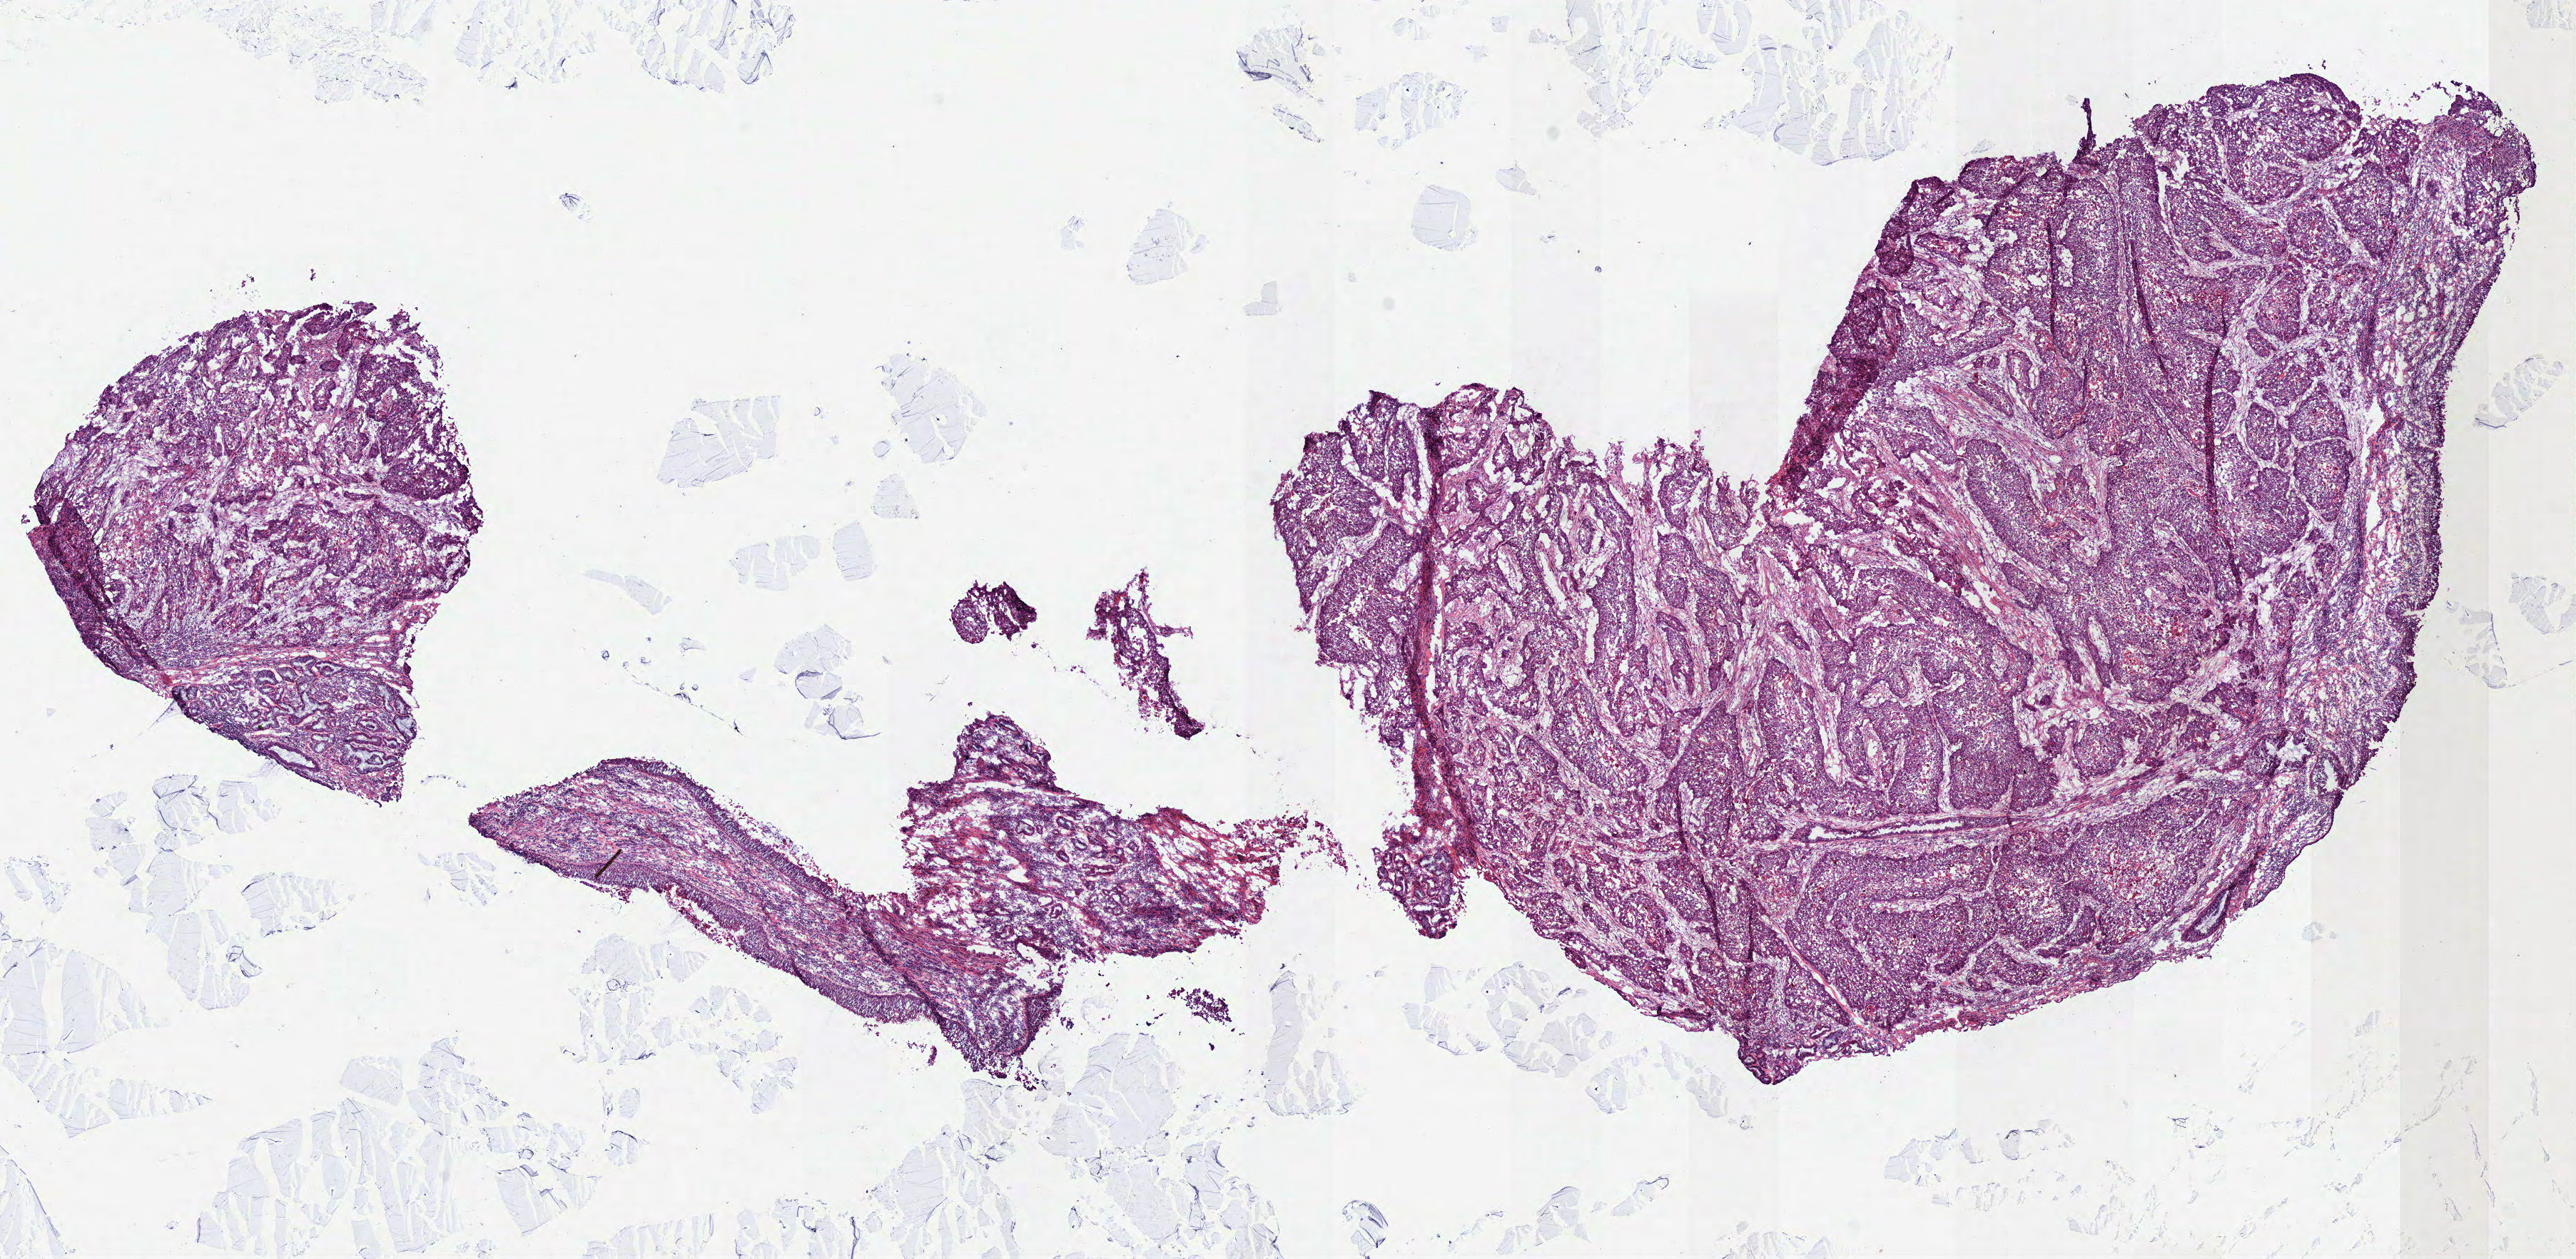
Whole-slide histology image, H&E-stained — low-resolution overview of the scanned area, about 14.2 x 6.9 mm, frozen section, head and neck, primary tumour sample. Patient: male, age at initial diagnosis 47 years. Histologic grade: G3 (poorly differentiated). Composition of this section per pathologist review: tumour cells 78%, tumour nuclei 75%, normal cells 12%, stromal cells 10%, necrosis 0%.
• histologic diagnosis: Squamous cell carcinoma, NOS (larynx, NOS)
• AJCC pathologic stage: IVA